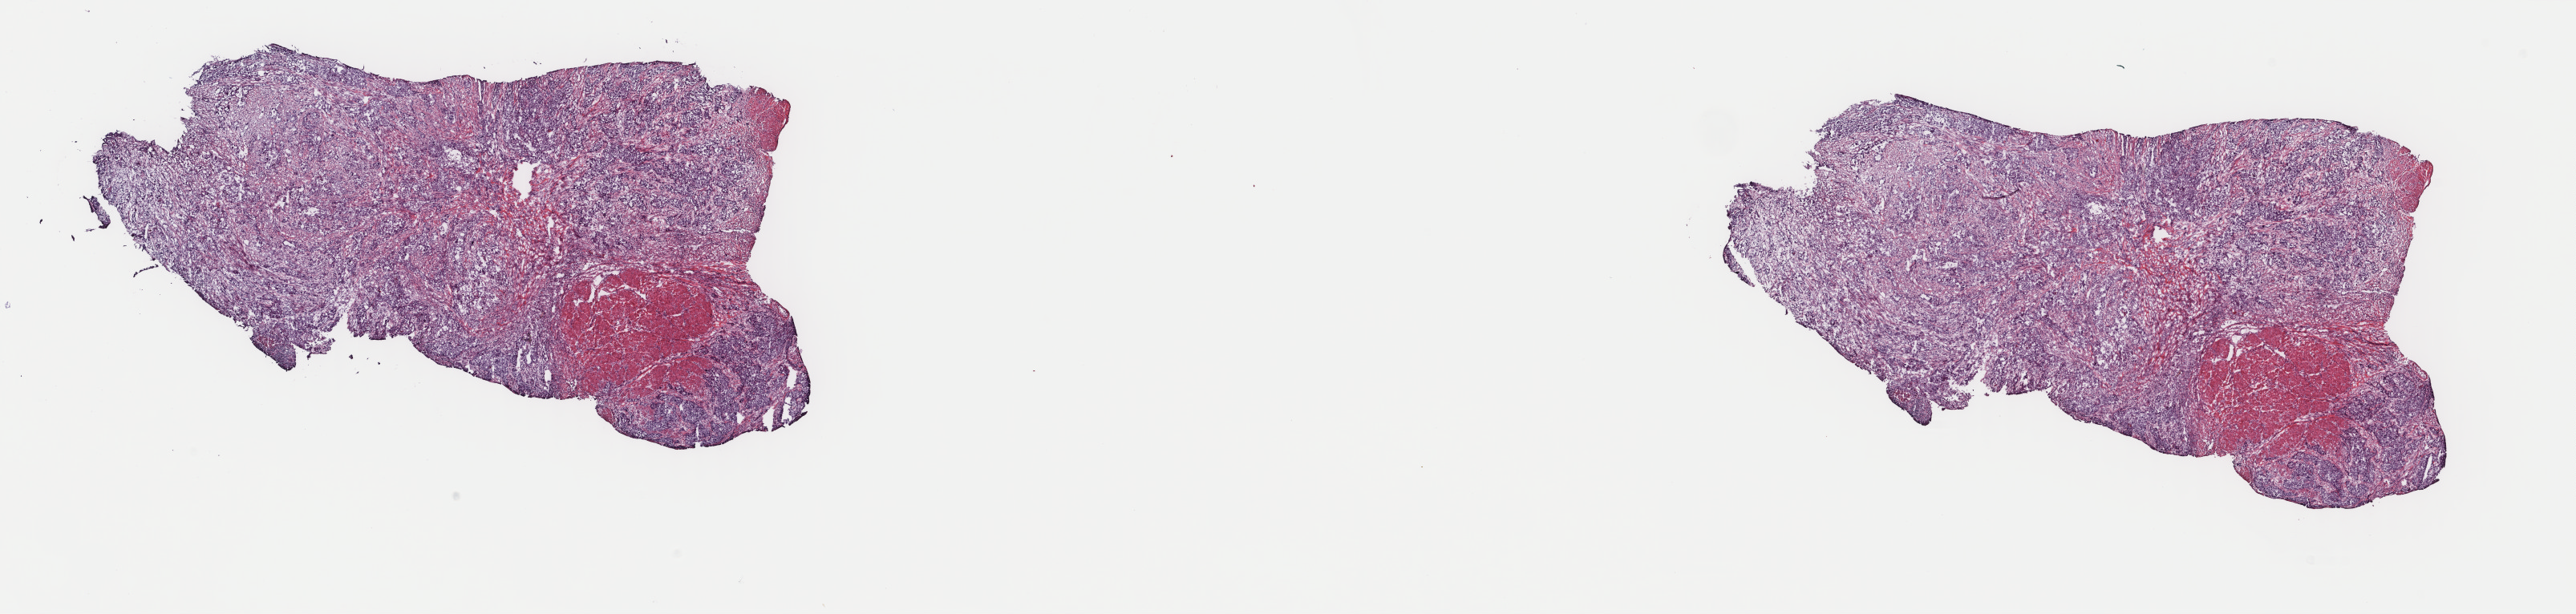
Hematoxylin and eosin (H&E) stained whole-slide image, a low-resolution overview of the entire scanned area, about 25.5 x 6.1 mm (acquisition: 40x scan). Frozen section. Bladder, primary tumour sample. Female patient; age at initial diagnosis 78 years. Histologic grade: high grade. Pathologist review of this section (percent, as recorded): tumour cells 90%, tumour nuclei 70%, normal cells 10%, stromal cells 0%, necrosis 0%. Inflammatory infiltration, as recorded: lymphocyte infiltration 5%, monocyte infiltration 0%, neutrophil infiltration 0%.
- lymph nodes positive (case pathology): 0 of 20 examined
- pathologic diagnosis: Transitional cell carcinoma (lateral wall of bladder)
- AJCC pathologic stage: III (7th edition)